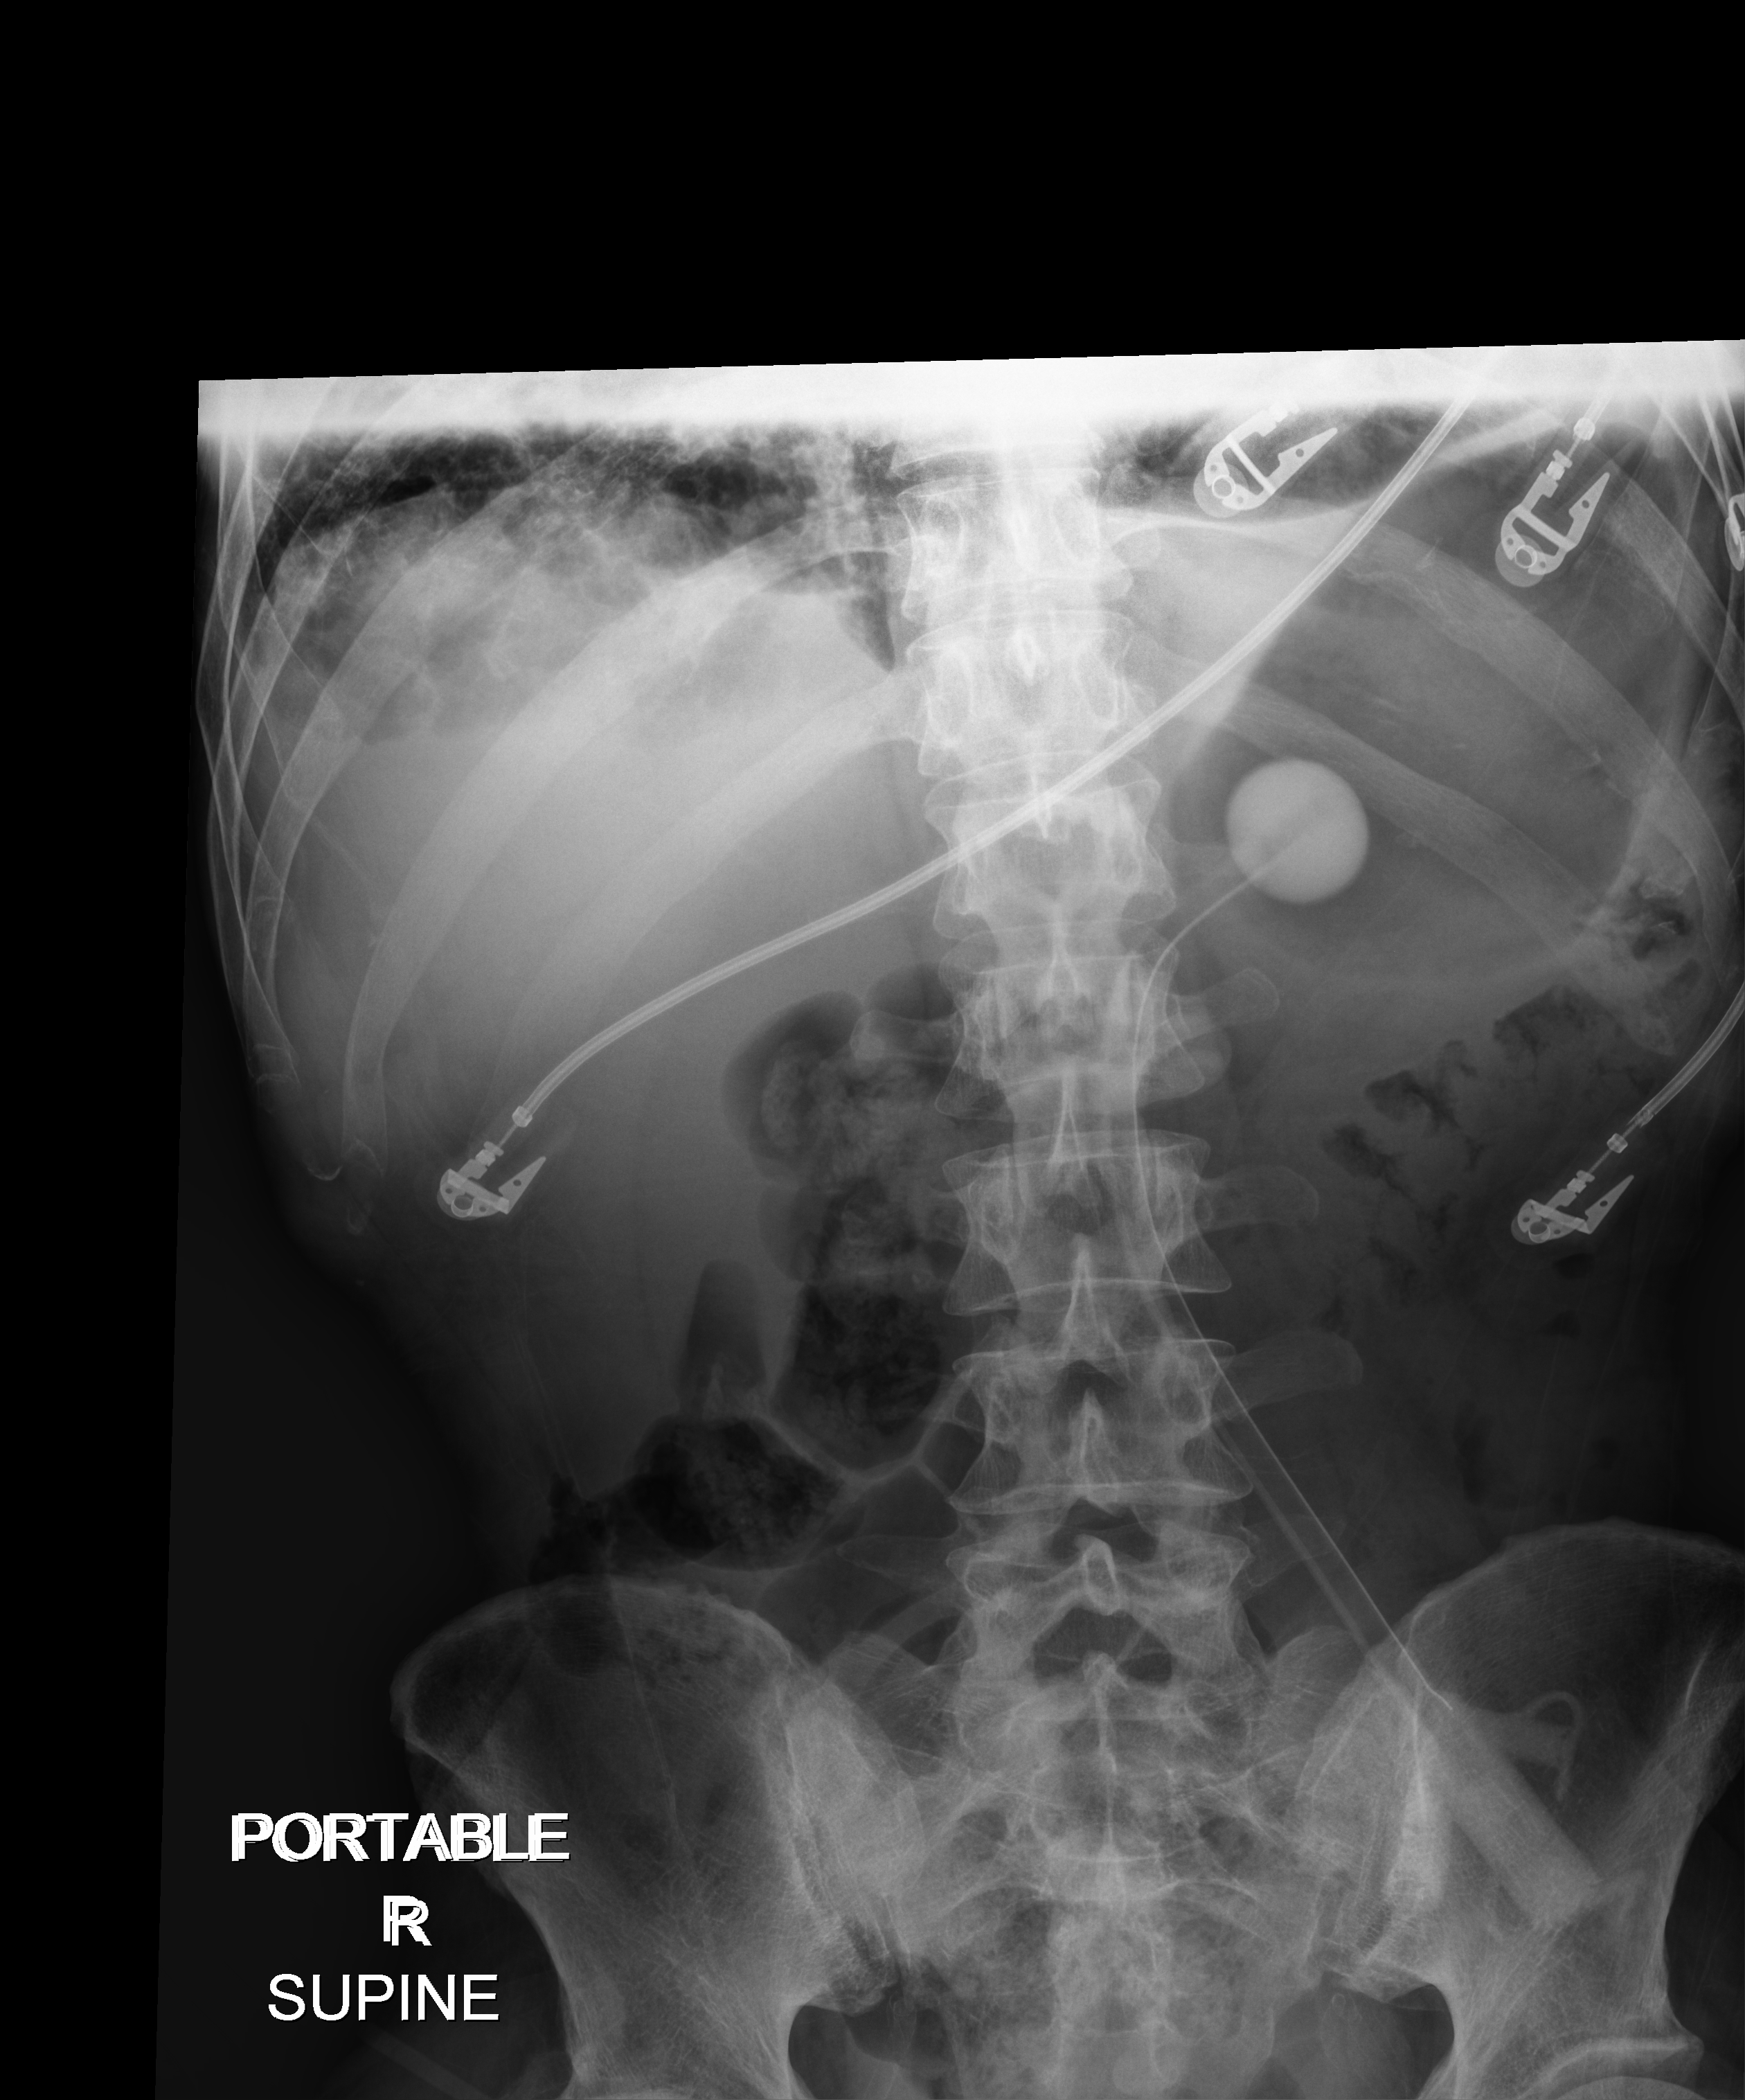
Abdomen X-ray (portable), anteroposterior (AP) projection. Patient hospitalised with COVID-19; male, aged 18–59 years.
From the hospital-stay record, not from the radiograph (when in the stay this image was taken is not recorded): mechanically ventilated during this hospital stay: yes; hypertension (admission record): yes.